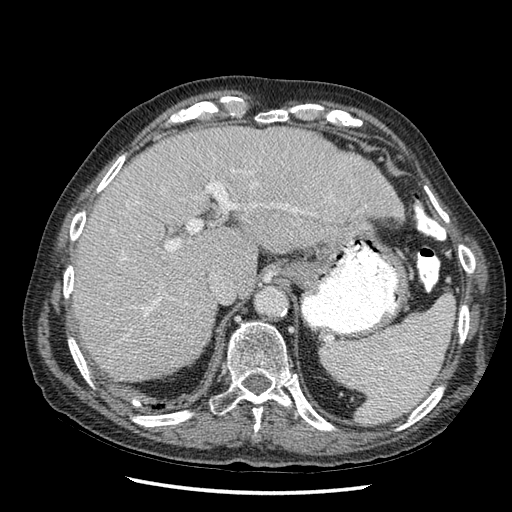
Contrast-enhanced abdominal CT (liver protocol), one axial slice; position 39 of 67 along the scan axis; soft-tissue window (W 400 / L 40 HU); 512 × 512 image matrix, field of view 360 × 360 mm. From the clinical record (not read from this slice): diagnosis: hepatocellular carcinoma (patient treated with transarterial chemoembolisation; whether this scan precedes or follows treatment is not stated here); TNM stage (as recorded): Stage-I; Child-Pugh class: A; tumour differentiation: moderately differentiated; tumour nodularity: uninodular.
Outlined on this slice (semi-automatic segmentation, software-assisted and operator-edited):
- liver parenchyma outside the tumour (the mass and vessels are separate outlines, so this box may not span the whole liver): bounding box (x1, y1, x2, y2) in pixels: (72, 126, 402, 380)
- liver vessels: (125, 169, 296, 311)